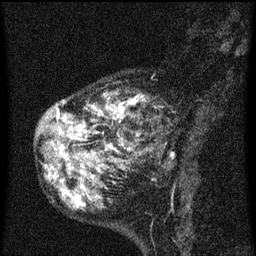
Breast MRI (dynamic contrast-enhanced), one sagittal slice. Slice 20 of 60 in the series (ordered by position). Dynamic contrast-enhanced series, image 2 of 3 at this slice position (ordered by acquisition). 1.5 T. TE 4.2 ms, TR 8 ms. 2 mm slice thickness. 256 × 256 image matrix. Female patient, age 55 years.
Structures marked on this image (semi-automatic segmentation, software-assisted and operator-edited):
- analysis volume of interest (the breast-tissue region the enhancement analysis was run in; not a lesion): box from (x=42, y=74) to (x=182, y=155) px
- tumour enhancement mask (voxels above the 70 % enhancement threshold inside the analysis volume of interest): (x=57, y=94)–(x=175, y=155)